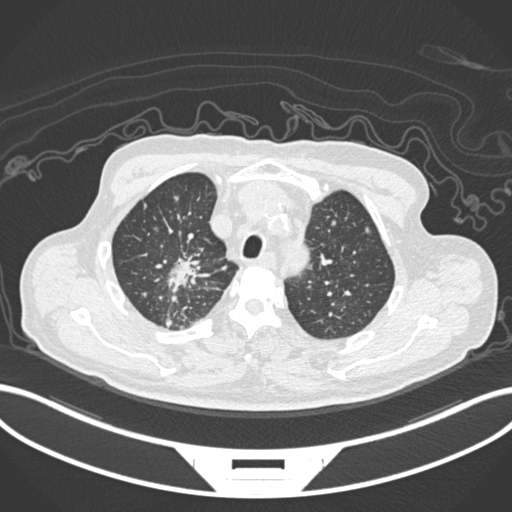
Chest CT, one axial slice; position 171 of 207 along the scan axis; reconstruction kernel B30f; lung window (W 1500 / L -600 HU); 512 × 512 image matrix, field of view 400 × 400 mm. Male patient, age 69 years. Case-level facts recorded for this patient, not image findings: clinical TNM (as recorded): T1c N1 M1.
Annotated regions visible in this slice (rectangle marked by the reading radiologist):
- lung tumour (recorded histology: adenocarcinoma): bounding box [x1, y1, x2, y2] px = [161, 251, 212, 297]